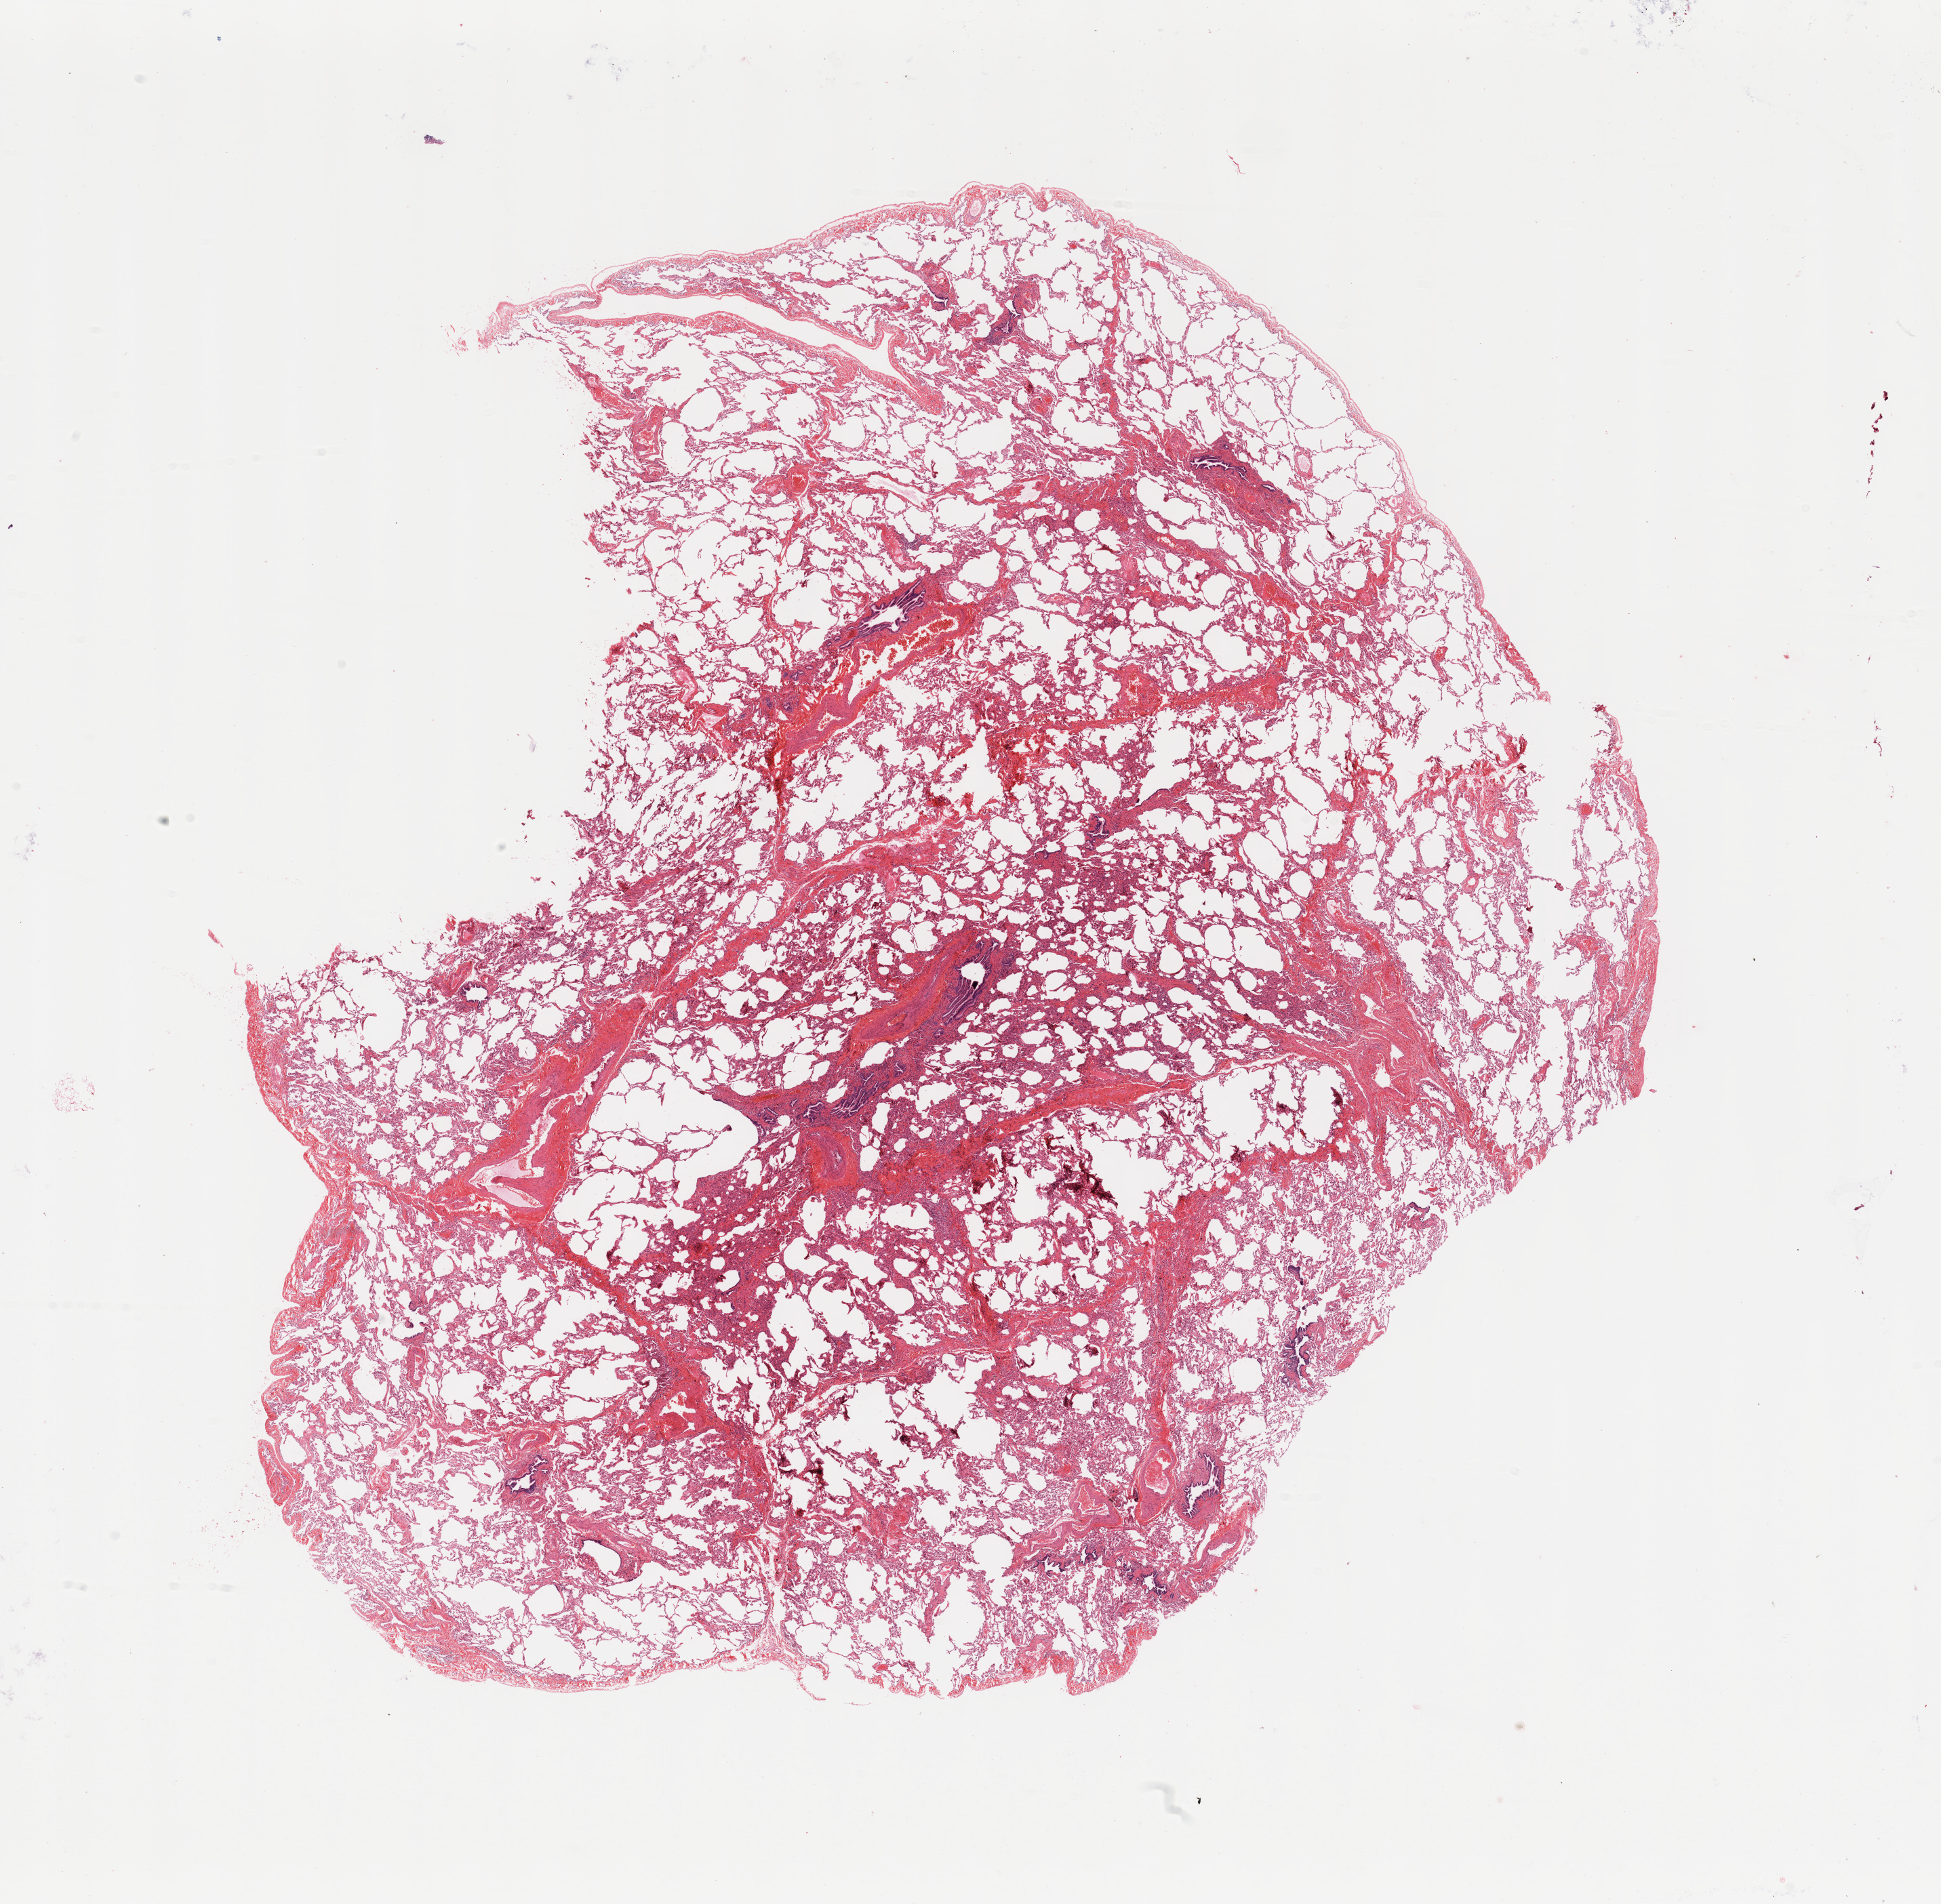
Hematoxylin and eosin (H&E) stained whole-slide image, whole scanned area (about 22.6 x 22.2 mm, slide scanned at 20x) shown as a low-resolution overview, normal (non-tumour) tissue sample, sampled site: lung. Female, 37 y/o.
• this section: normal (non-tumour) tissue from the same patient
• patient diagnosis: Adenocarcinoma, NOS